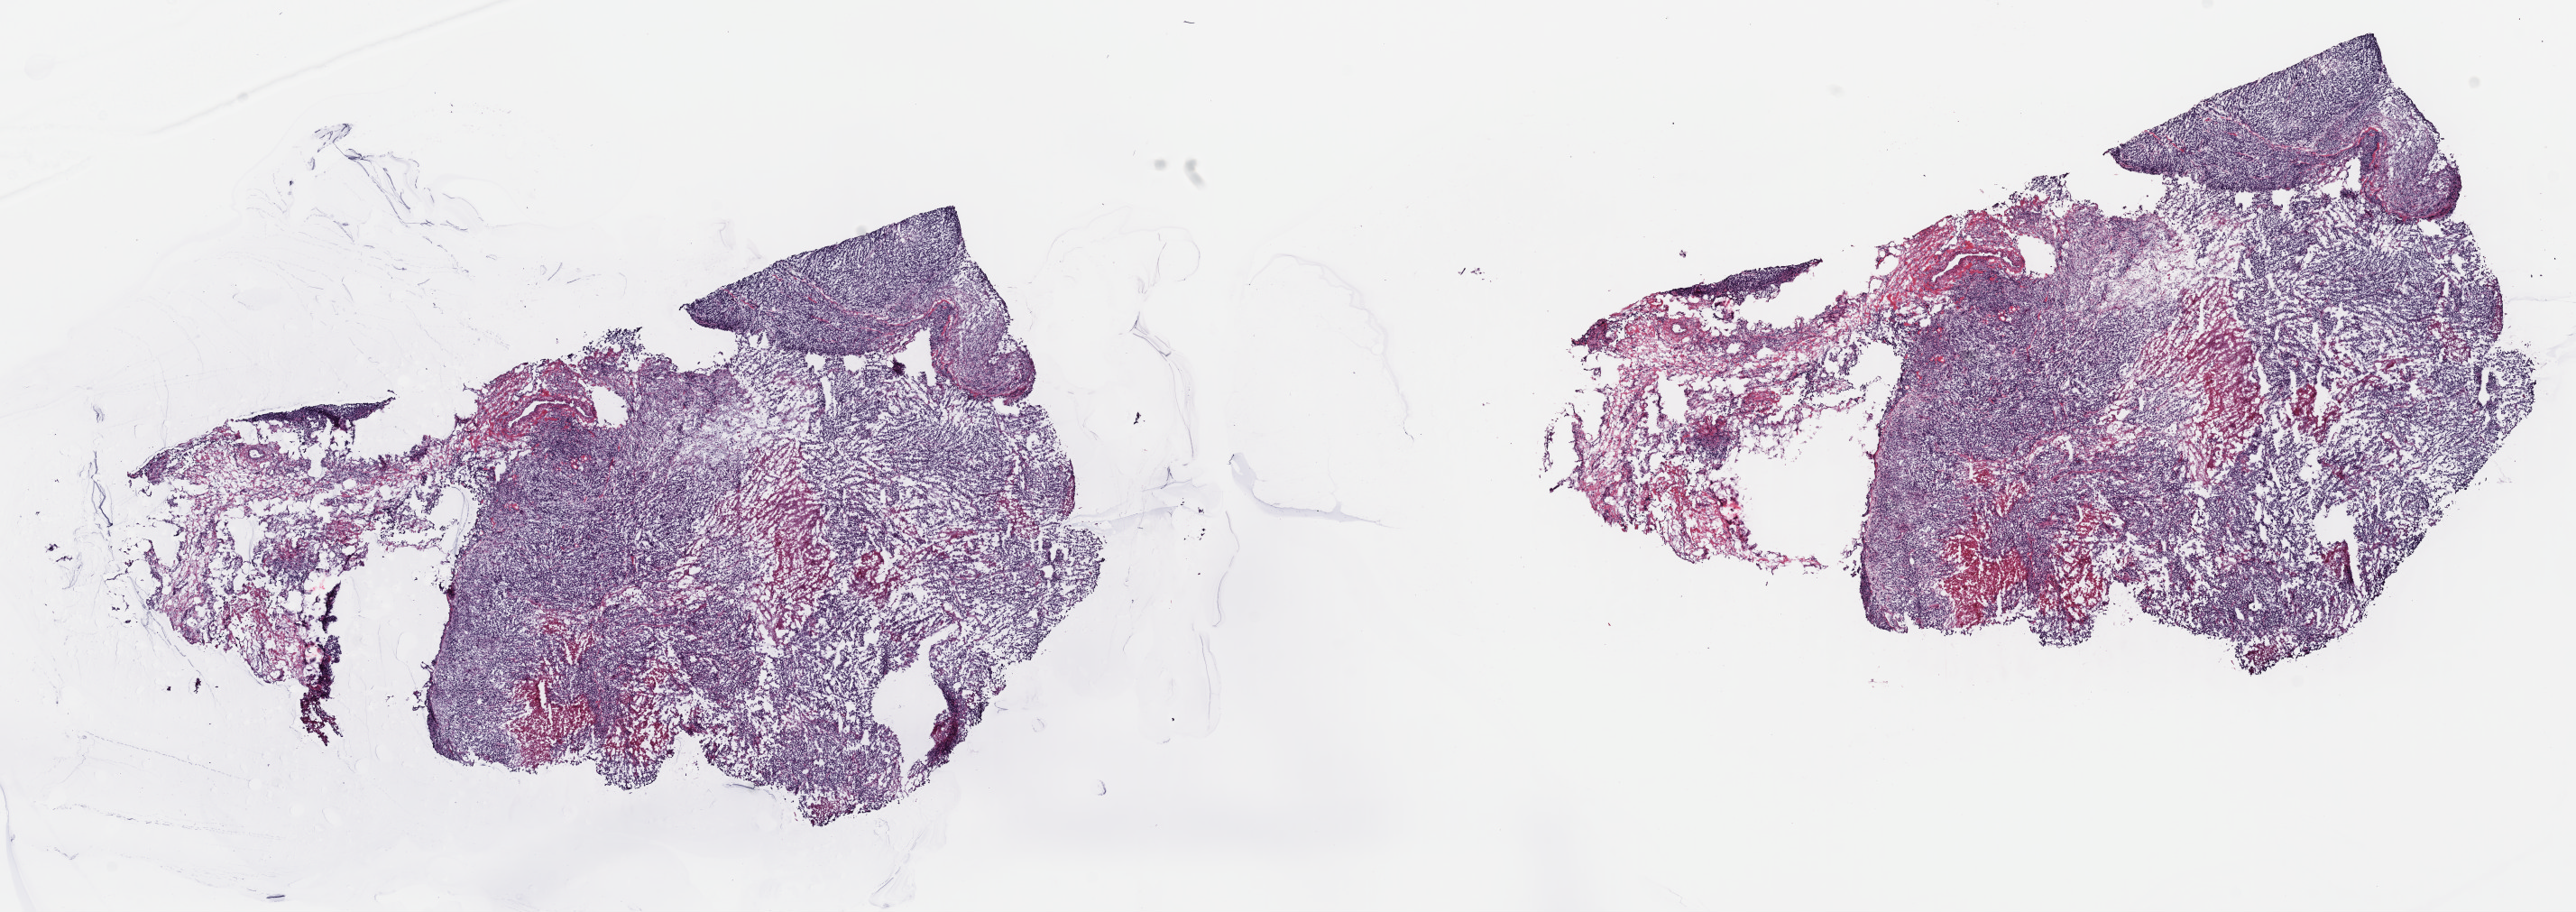
Digitized H&E-stained tissue section (whole slide) — a low-resolution overview of the entire scanned area, about 22.5 x 8.0 mm (slide scanned at 40x); frozen section from the top of the tissue portion; metastatic tumour sample, sampled site: lymph node. Female, age 45 years at initial diagnosis. Pathologist review of this section (percent, as recorded): tumour cells 70%, tumour nuclei 70%, normal cells 0%, stromal cells 20%, necrosis 10%. Infiltration values recorded for this section: lymphocyte infiltration 3%, monocyte infiltration 2%, neutrophil infiltration 1%.
This section: metastatic tumour tissue. Patient diagnosis: Malignant melanoma, NOS.